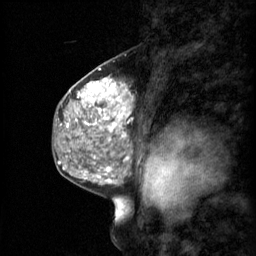
Breast MRI (dynamic contrast-enhanced), one sagittal slice; slice 35 of 60 in the series (ordered by position); 3 images stored at this slice position (order not interpretable as contrast timing); 1.5 T; TE 4.2 ms, TR 11 ms; 2 mm slice thickness; 256 × 256 image matrix. Patient: female, 48 years.
Outlined on this slice (semi-automatically segmented with operator editing):
- analysis volume of interest (the breast-tissue region the enhancement analysis was run in; not a lesion): bounding box <69,74,136,147> (left, top, right, bottom; pixels)
- tumour enhancement mask (voxels above the 70 % enhancement threshold inside the analysis volume of interest): <78,78,133,141>